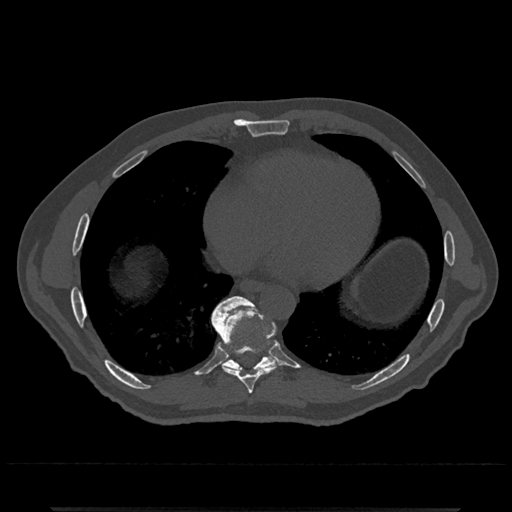
CT including the spine, one axial slice; position 646 of 797 along the scan axis; reconstruction kernel Br40s/3; 120 kVp; bone window (W 1800 / L 400 HU); 0.5 mm slice thickness; 512 × 512 image matrix, field of view 393 × 393 mm. Patient: male, 67 years. Case-level facts recorded for this patient, not image findings: primary cancer: prostate.
Annotated regions visible in this slice (semi-automatically segmented with operator editing):
- T8 vertebra: bounding box (x1, y1, x2, y2) in pixels: (212, 308, 280, 394)
- T9 vertebra: (211, 296, 276, 371)